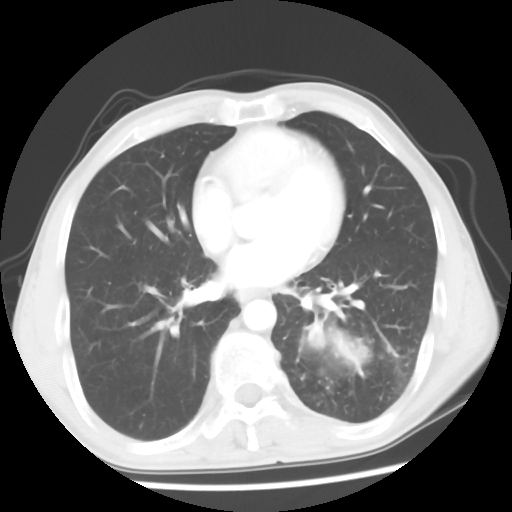
Chest CT, one axial slice. Reconstruction kernel STANDARD. Lung window (W 1500 / L -600 HU). 5 mm slice thickness. 512 × 512 image matrix. Male patient, age 60 years. Case-level facts recorded for this patient, not image findings: clinical TNM (as recorded): T4 N0 M0.
Outlined on this slice (rectangle marked by the reading radiologist):
- lung tumour (recorded histology: squamous cell carcinoma): bounding box [x1, y1, x2, y2] px = [304, 305, 384, 383]